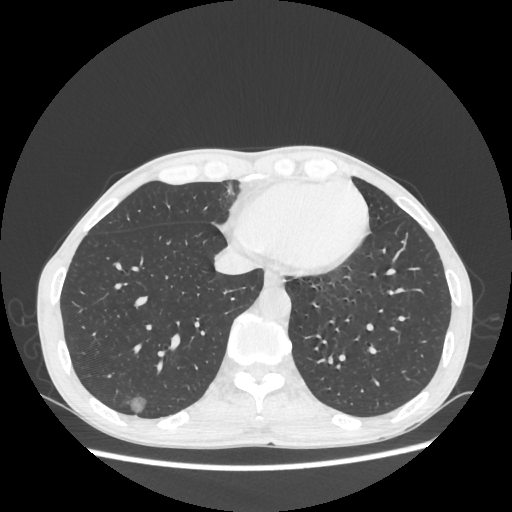
Chest CT, one axial slice; slice 78 of 270 in the series (ordered by position); lung window (W 1500 / L -600 HU); 1.25 mm slice thickness; 512 × 512 image matrix. Patient: male, 60 years. From the clinical record (not read from this slice): clinical TNM (as recorded): T1c N0 M0; histopathological grade: G2.
Structures marked on this image (rectangle marked by the reading radiologist):
- lung tumour (recorded histology: adenocarcinoma): bounding box (x1, y1, x2, y2) in pixels: (119, 386, 155, 419)